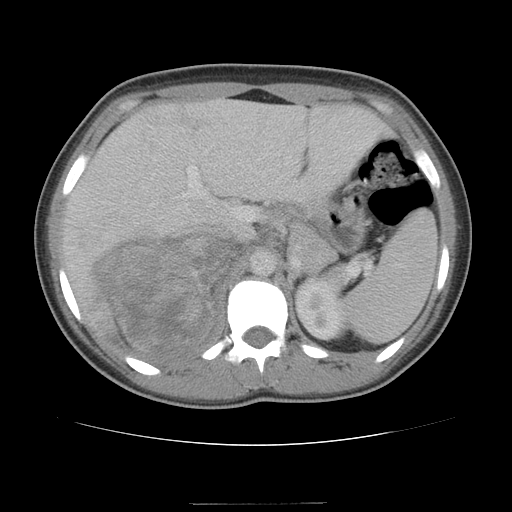
Contrast-enhanced abdominal CT, one axial slice. Position 74 of 100 along the scan axis. Reconstruction kernel STANDARD. 120 kVp. Intravenous contrast given. Soft-tissue window (W 400 / L 40 HU). 512 × 512 image matrix. Patient: female, 21 years. From the clinical record (not read from this slice): diagnosis: adrenocortical carcinoma; tumour side: right adrenal; tumour size at pathology: 15.5 cm; Ki-67 index: 26 %; stage (as recorded): 3.
Outlined on this slice (semi-automatically segmented with operator editing):
- mass: bounding box (x1, y1, x2, y2) in pixels: (92, 233, 247, 359)